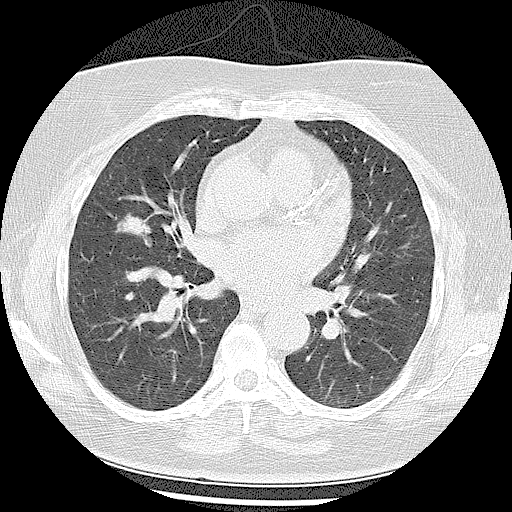
Axial slice from a low-dose chest CT screening exam, baseline screening round, lung window (W 1500 / L -600 HU), 2.5 mm slice thickness, slice 53 of 102 in the series. Female participant, aged 57 years at enrolment.
Expert-annotated lung lesion, bounding box <104,200,167,255> (left, top, right, bottom; pixels). The screening reader recorded 4 non-calcified nodules or masses ≥4 mm on this exam; which of them this box marks is not recorded. Official screen result: positive, change unspecified: nodule(s) >= 4 mm or enlarging nodule(s), mass(es), or other non-specific abnormalities suspicious for lung cancer. Lung cancer was diagnosed 87 days after this screen: adenocarcinoma, NOS, right middle lobe, well differentiated (G1), stage IA (AJCC 6th edition), 21 mm at pathology.